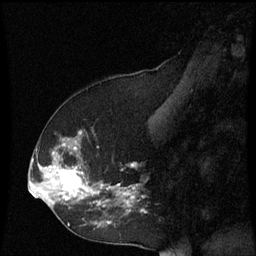
Breast MRI (dynamic contrast-enhanced), one sagittal slice; position 29 of 60 along the scan axis; dynamic contrast-enhanced series, image 2 of 3 at this slice position (ordered by acquisition); 1.5 T; TE 4.2 ms, TR 8.9 ms; 2 mm slice thickness; 256 × 256 image matrix. Female patient, age 53 years. From the clinical record (not read from this slice): setting: breast cancer imaged before/during neoadjuvant chemotherapy; receptor status: HR-positive, HER2-negative.
Structures marked on this image (semi-automatically segmented with operator editing):
- analysis volume of interest (the breast-tissue region the enhancement analysis was run in; not a lesion): bounding box (x1, y1, x2, y2) in pixels: (38, 130, 149, 231)
- tumour enhancement mask (voxels above the 70 % enhancement threshold inside the analysis volume of interest): (38, 132, 145, 225)